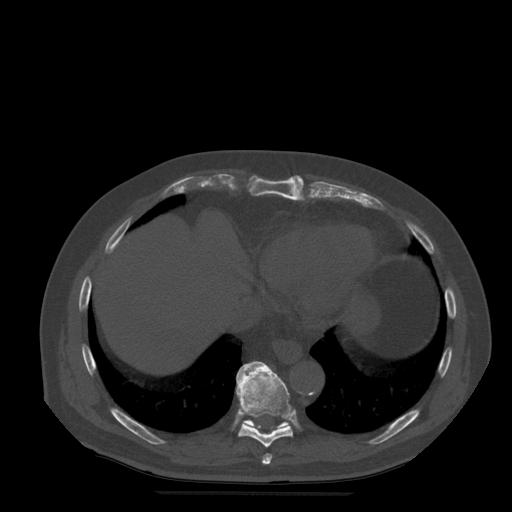
CT including the spine, one axial slice. Slice 285 of 522 in the series (ordered by position). Bone window (W 1800 / L 400 HU). 1.25 mm slice thickness. 512 × 512 image matrix, field of view 420 × 420 mm. Patient age 72 years. From the clinical record (not read from this slice): primary cancer: prostate.
Outlined on this slice (semi-automatic segmentation, software-assisted and operator-edited):
- T10 vertebra: bounding box [x1, y1, x2, y2] px = [240, 361, 289, 431]
- T8 vertebra: [262, 454, 273, 465]
- T9 vertebra: [236, 362, 294, 448]